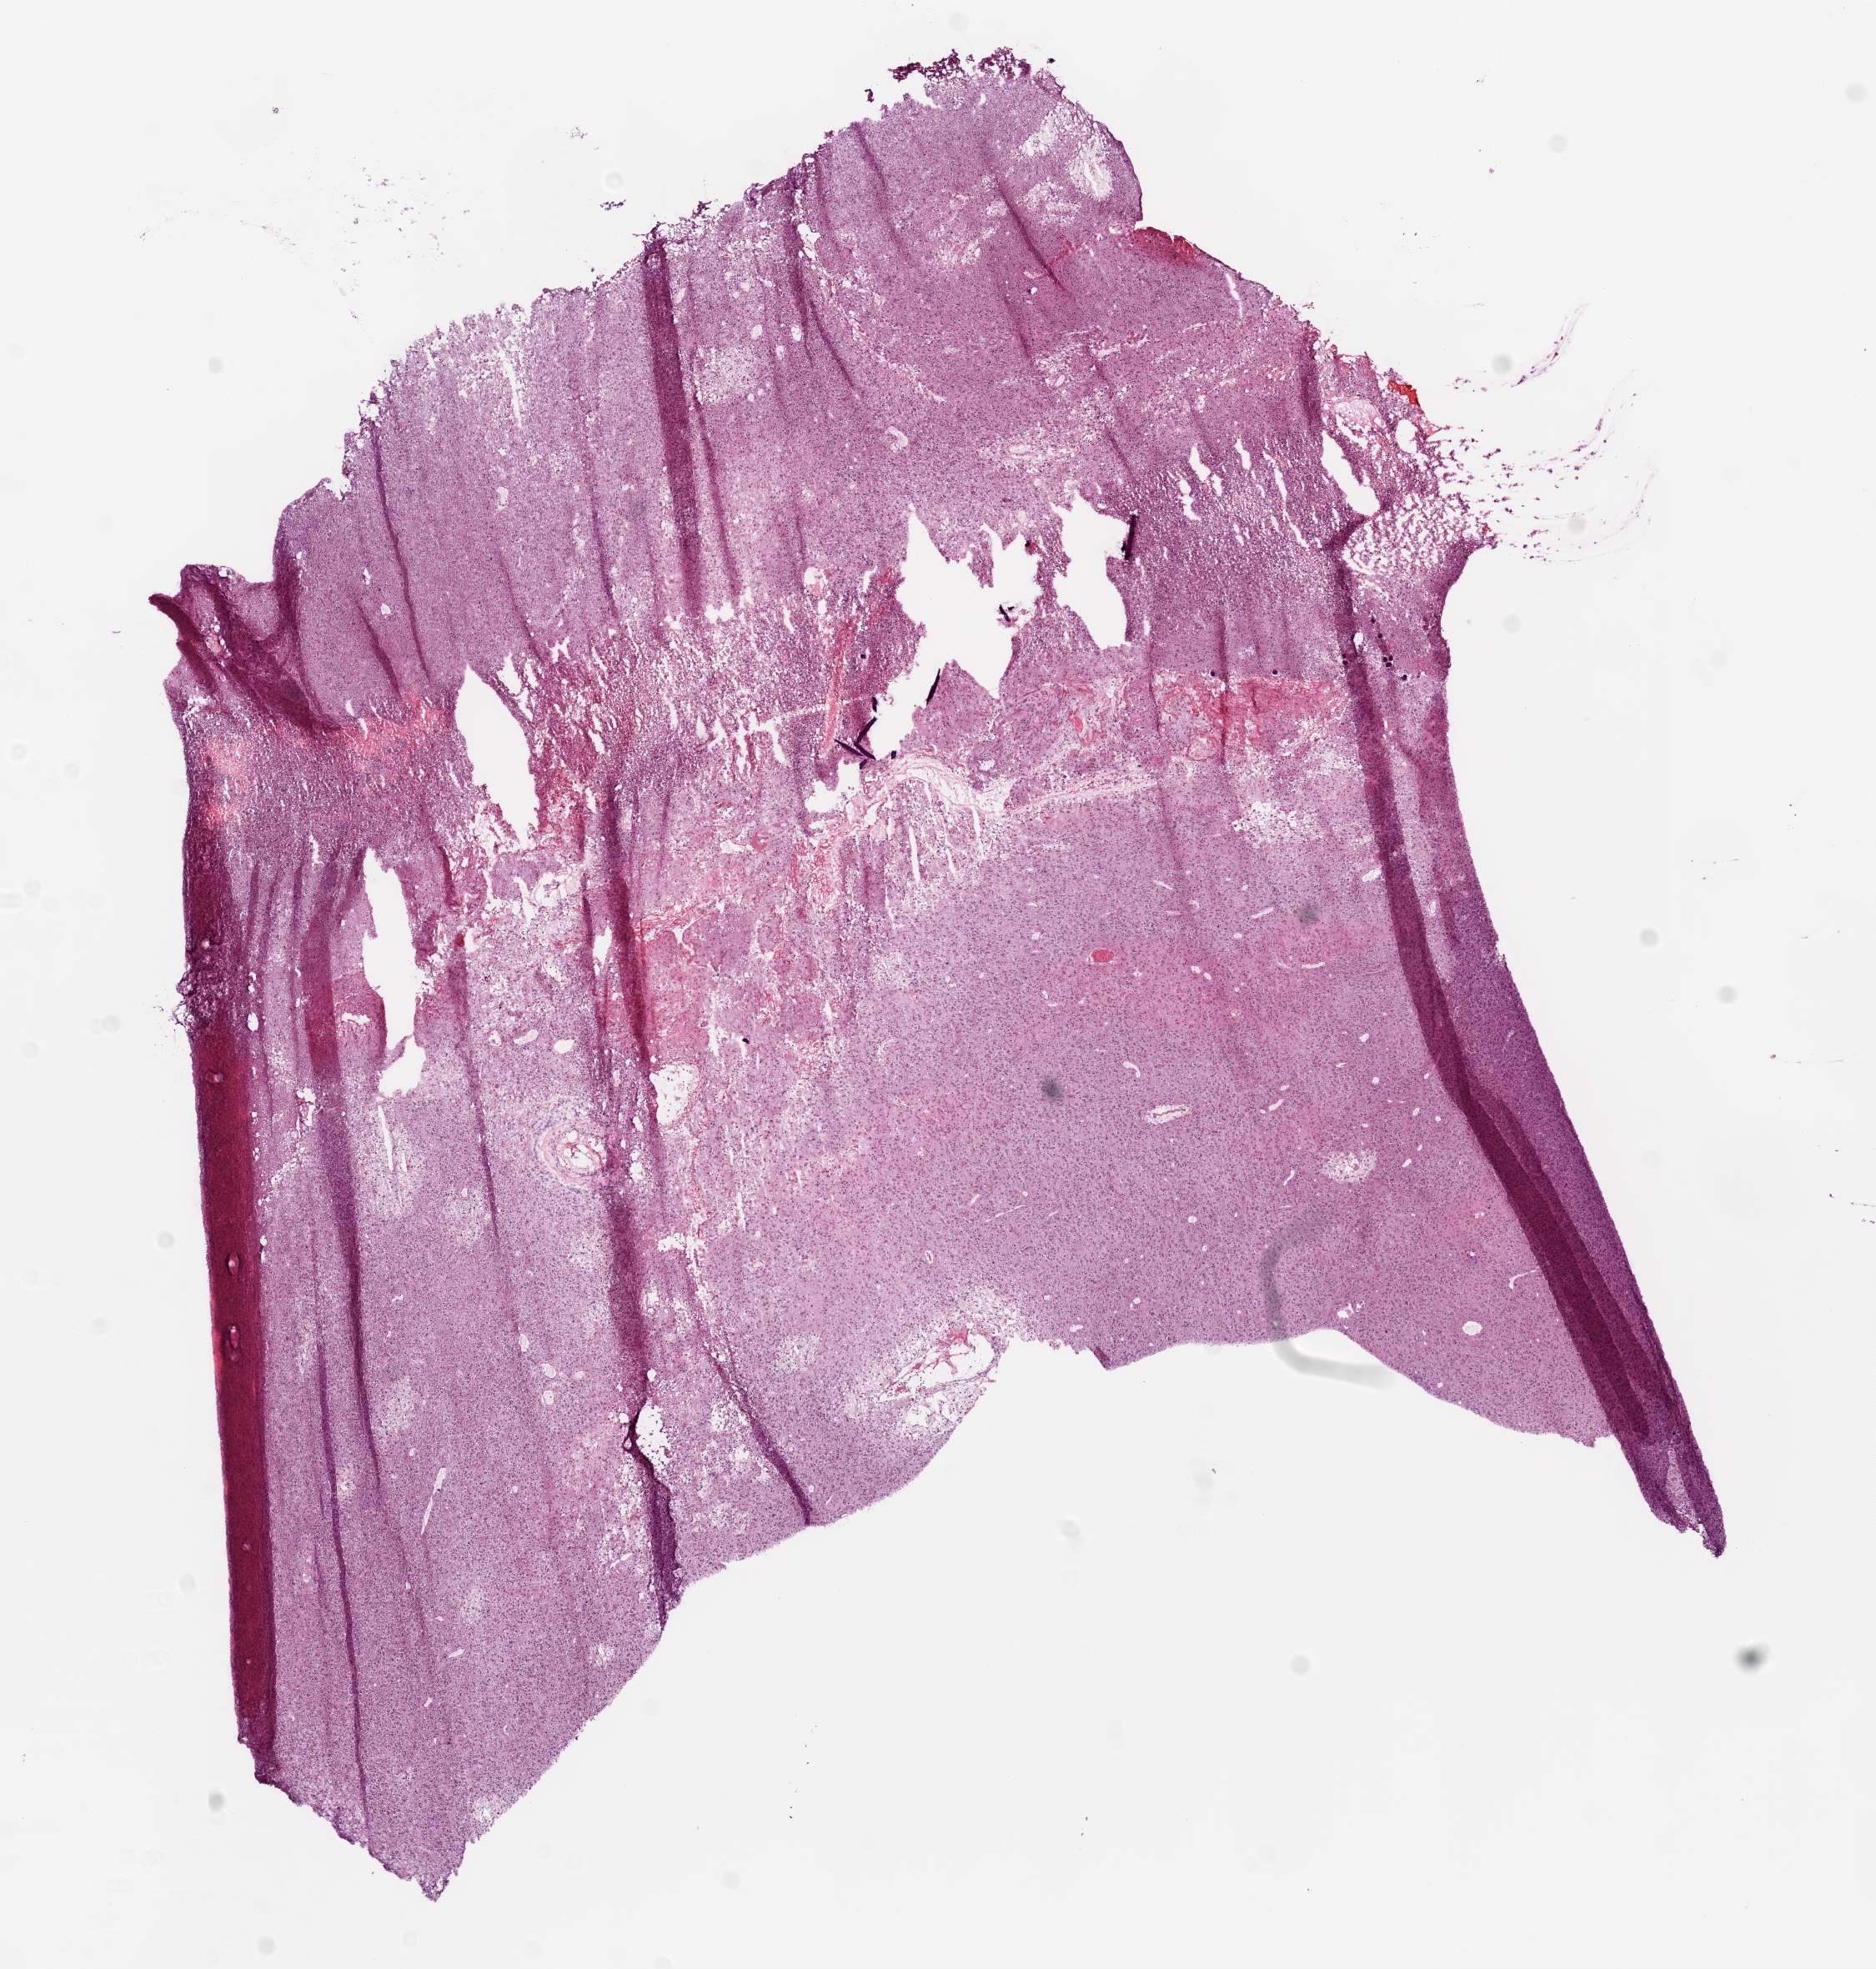
Whole-slide histology image, Hematoxylin and eosin (H&E) stained, a low-resolution overview of the entire scanned area, about 9.0 x 9.5 mm; frozen section from the bottom of the tissue portion; primary tumour sample from the brain. Male, age 60 years at initial diagnosis. Composition of this section per pathologist review: tumour cells 90%, tumour nuclei 90%, normal cells 0%, stromal cells 5%, necrosis 5%.
Histologic diagnosis: Glioblastoma.